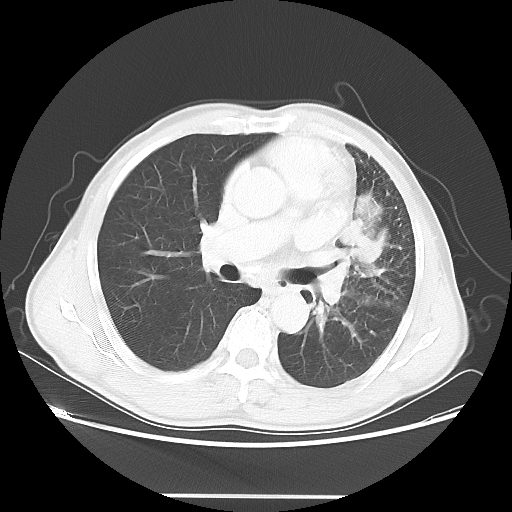
Chest CT, one axial slice; position 29 of 55 along the scan axis; reconstruction kernel LUNG; 100 kVp; lung window (W 1500 / L -600 HU); 5 mm slice thickness; 512 × 512 image matrix. Patient: male, 60 years. Case-level facts recorded for this patient, not image findings: clinical TNM (as recorded): T3 N3 M0.
Structures marked on this image (rectangle marked by the reading radiologist):
- lung tumour (recorded histology: adenocarcinoma): box from (x=343, y=208) to (x=389, y=270) px